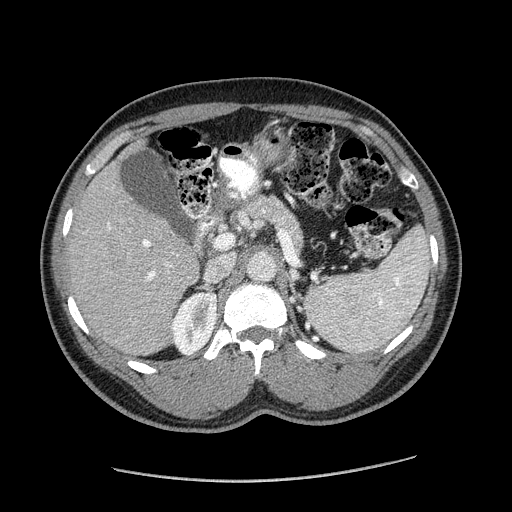
Contrast-enhanced abdominal CT (liver protocol), one axial slice. Position 103 of 182 along the scan axis. Soft-tissue window (W 400 / L 40 HU). 2.5 mm slice thickness. 512 × 512 image matrix. From the clinical record (not read from this slice): diagnosis: hepatocellular carcinoma (patient treated with transarterial chemoembolisation; whether this scan precedes or follows treatment is not stated here); TNM stage (as recorded): Stage-I; Child-Pugh class: A.
Outlined on this slice (semi-automatically segmented with operator editing):
- liver parenchyma outside the tumour (the mass and vessels are separate outlines, so this box may not span the whole liver): bounding box <68,140,198,354> (left, top, right, bottom; pixels)
- mass: <100,232,132,271>
- liver vessels: <107,223,172,282>